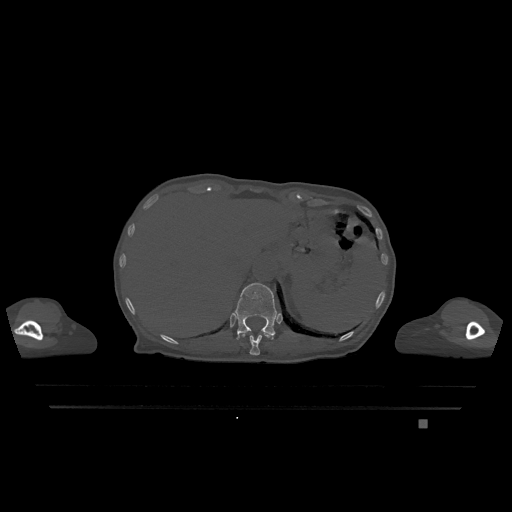
CT including the spine, one axial slice; slice 552 of 1317 in the series (ordered by position); bone window (W 1800 / L 400 HU); 0.5 mm slice thickness; 512 × 512 image matrix, field of view 500 × 500 mm. Female patient, age 74 years. From the clinical record (not read from this slice): primary cancer: lung; vertebrae with lytic lesions (as recorded): T1, T4, T5, T6, L4, L5.
Annotated regions visible in this slice (semi-automatic segmentation, software-assisted and operator-edited):
- T11 vertebra: bounding box <241,333,272,355> (left, top, right, bottom; pixels)
- T12 vertebra: <235,283,278,340>